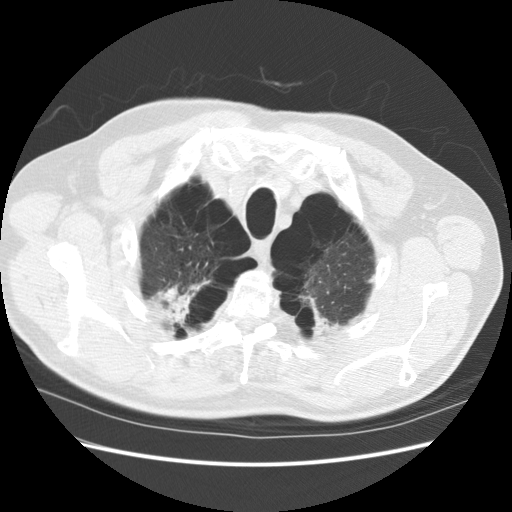
Axial slice from a low-dose chest CT screening exam, baseline screening round, lung window (W 1500 / L -600 HU), 2.5 mm slice thickness, standard (soft-tissue) reconstruction kernel (STANDARD). Male participant, aged 68 years at enrolment. Former smoker at enrolment.
Expert reader's lesion annotation, box from (x=129, y=268) to (x=218, y=334) px. The screening reader recorded 2 non-calcified nodules or masses ≥4 mm on this exam; which of them this box marks is not recorded.